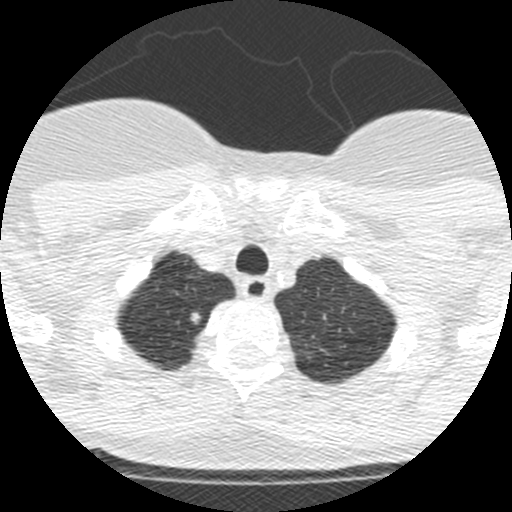
Low-dose screening chest CT, one axial slice. Slice 218 of 250 in the series (ordered by position). 120 kVp. Lung window (W 1500 / L -600 HU). 1.25 mm slice thickness. 512 × 512 image matrix, field of view 257 × 257 mm.
Outlined on this slice (manually delineated by an expert):
- lesion 1 (tumor, upper lobe of right lung): box from (x=190, y=312) to (x=201, y=324) px